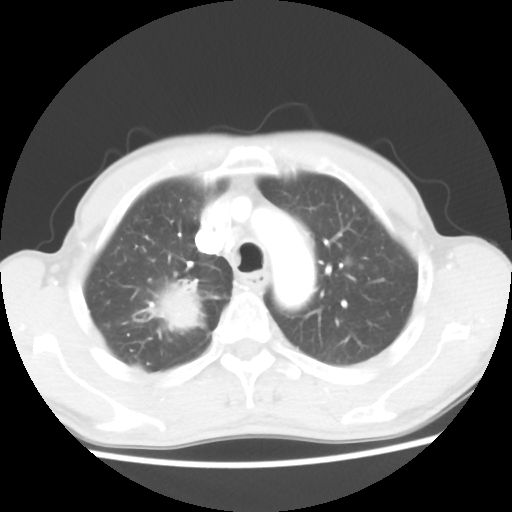
Chest CT, one axial slice. Position 41 of 52 along the scan axis. Reconstruction kernel STANDARD. 100 kVp. Lung window (W 1500 / L -600 HU). 5 mm slice thickness. 512 × 512 image matrix. Male patient, age 66 years. From the clinical record (not read from this slice): clinical TNM (as recorded): T2 N0 M1a.
Outlined on this slice (rectangle marked by the reading radiologist):
- lung tumour (recorded histology: adenocarcinoma): box from (x=143, y=276) to (x=214, y=337) px